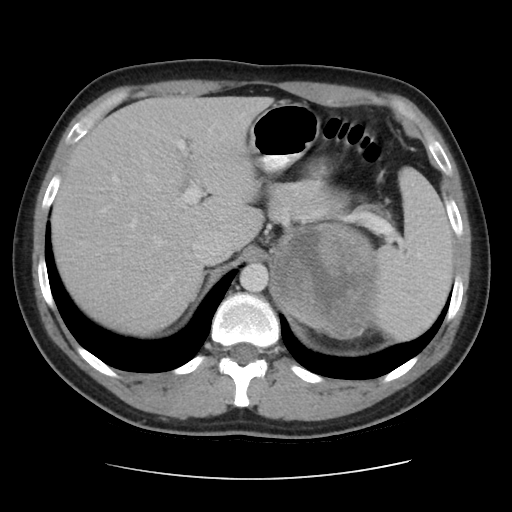
Contrast-enhanced abdominal CT, one axial slice. Slice 33 of 48 in the series (ordered by position). Intravenous contrast given. Soft-tissue window (W 400 / L 40 HU). 5 mm slice thickness. 512 × 512 image matrix, field of view 360 × 360 mm. Male patient, age 32 years. From the clinical record (not read from this slice): diagnosis: adrenocortical carcinoma; tumour side: left adrenal; tumour size at pathology: 14 cm; Ki-67 index: 67 %; stage (as recorded): 3.
Structures marked on this image (semi-automatically segmented with operator editing):
- mass: bounding box (x1, y1, x2, y2) in pixels: (277, 225, 372, 336)